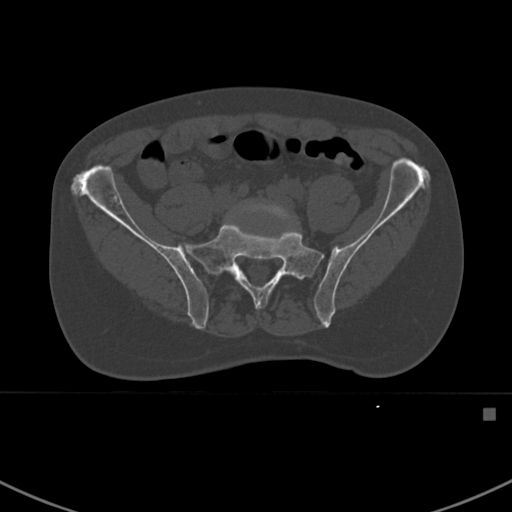
CT including the spine, one axial slice; slice 204 of 412 in the series (ordered by position); reconstruction kernel Br40s; 120 kVp; bone window (W 1800 / L 400 HU); 1.5 mm slice thickness; 512 × 512 image matrix. Patient: male, 59 years. Case-level facts recorded for this patient, not image findings: primary cancer: prostate.
Outlined on this slice (semi-automatic segmentation, software-assisted and operator-edited):
- L5 vertebra: bounding box <239,201,295,228> (left, top, right, bottom; pixels)